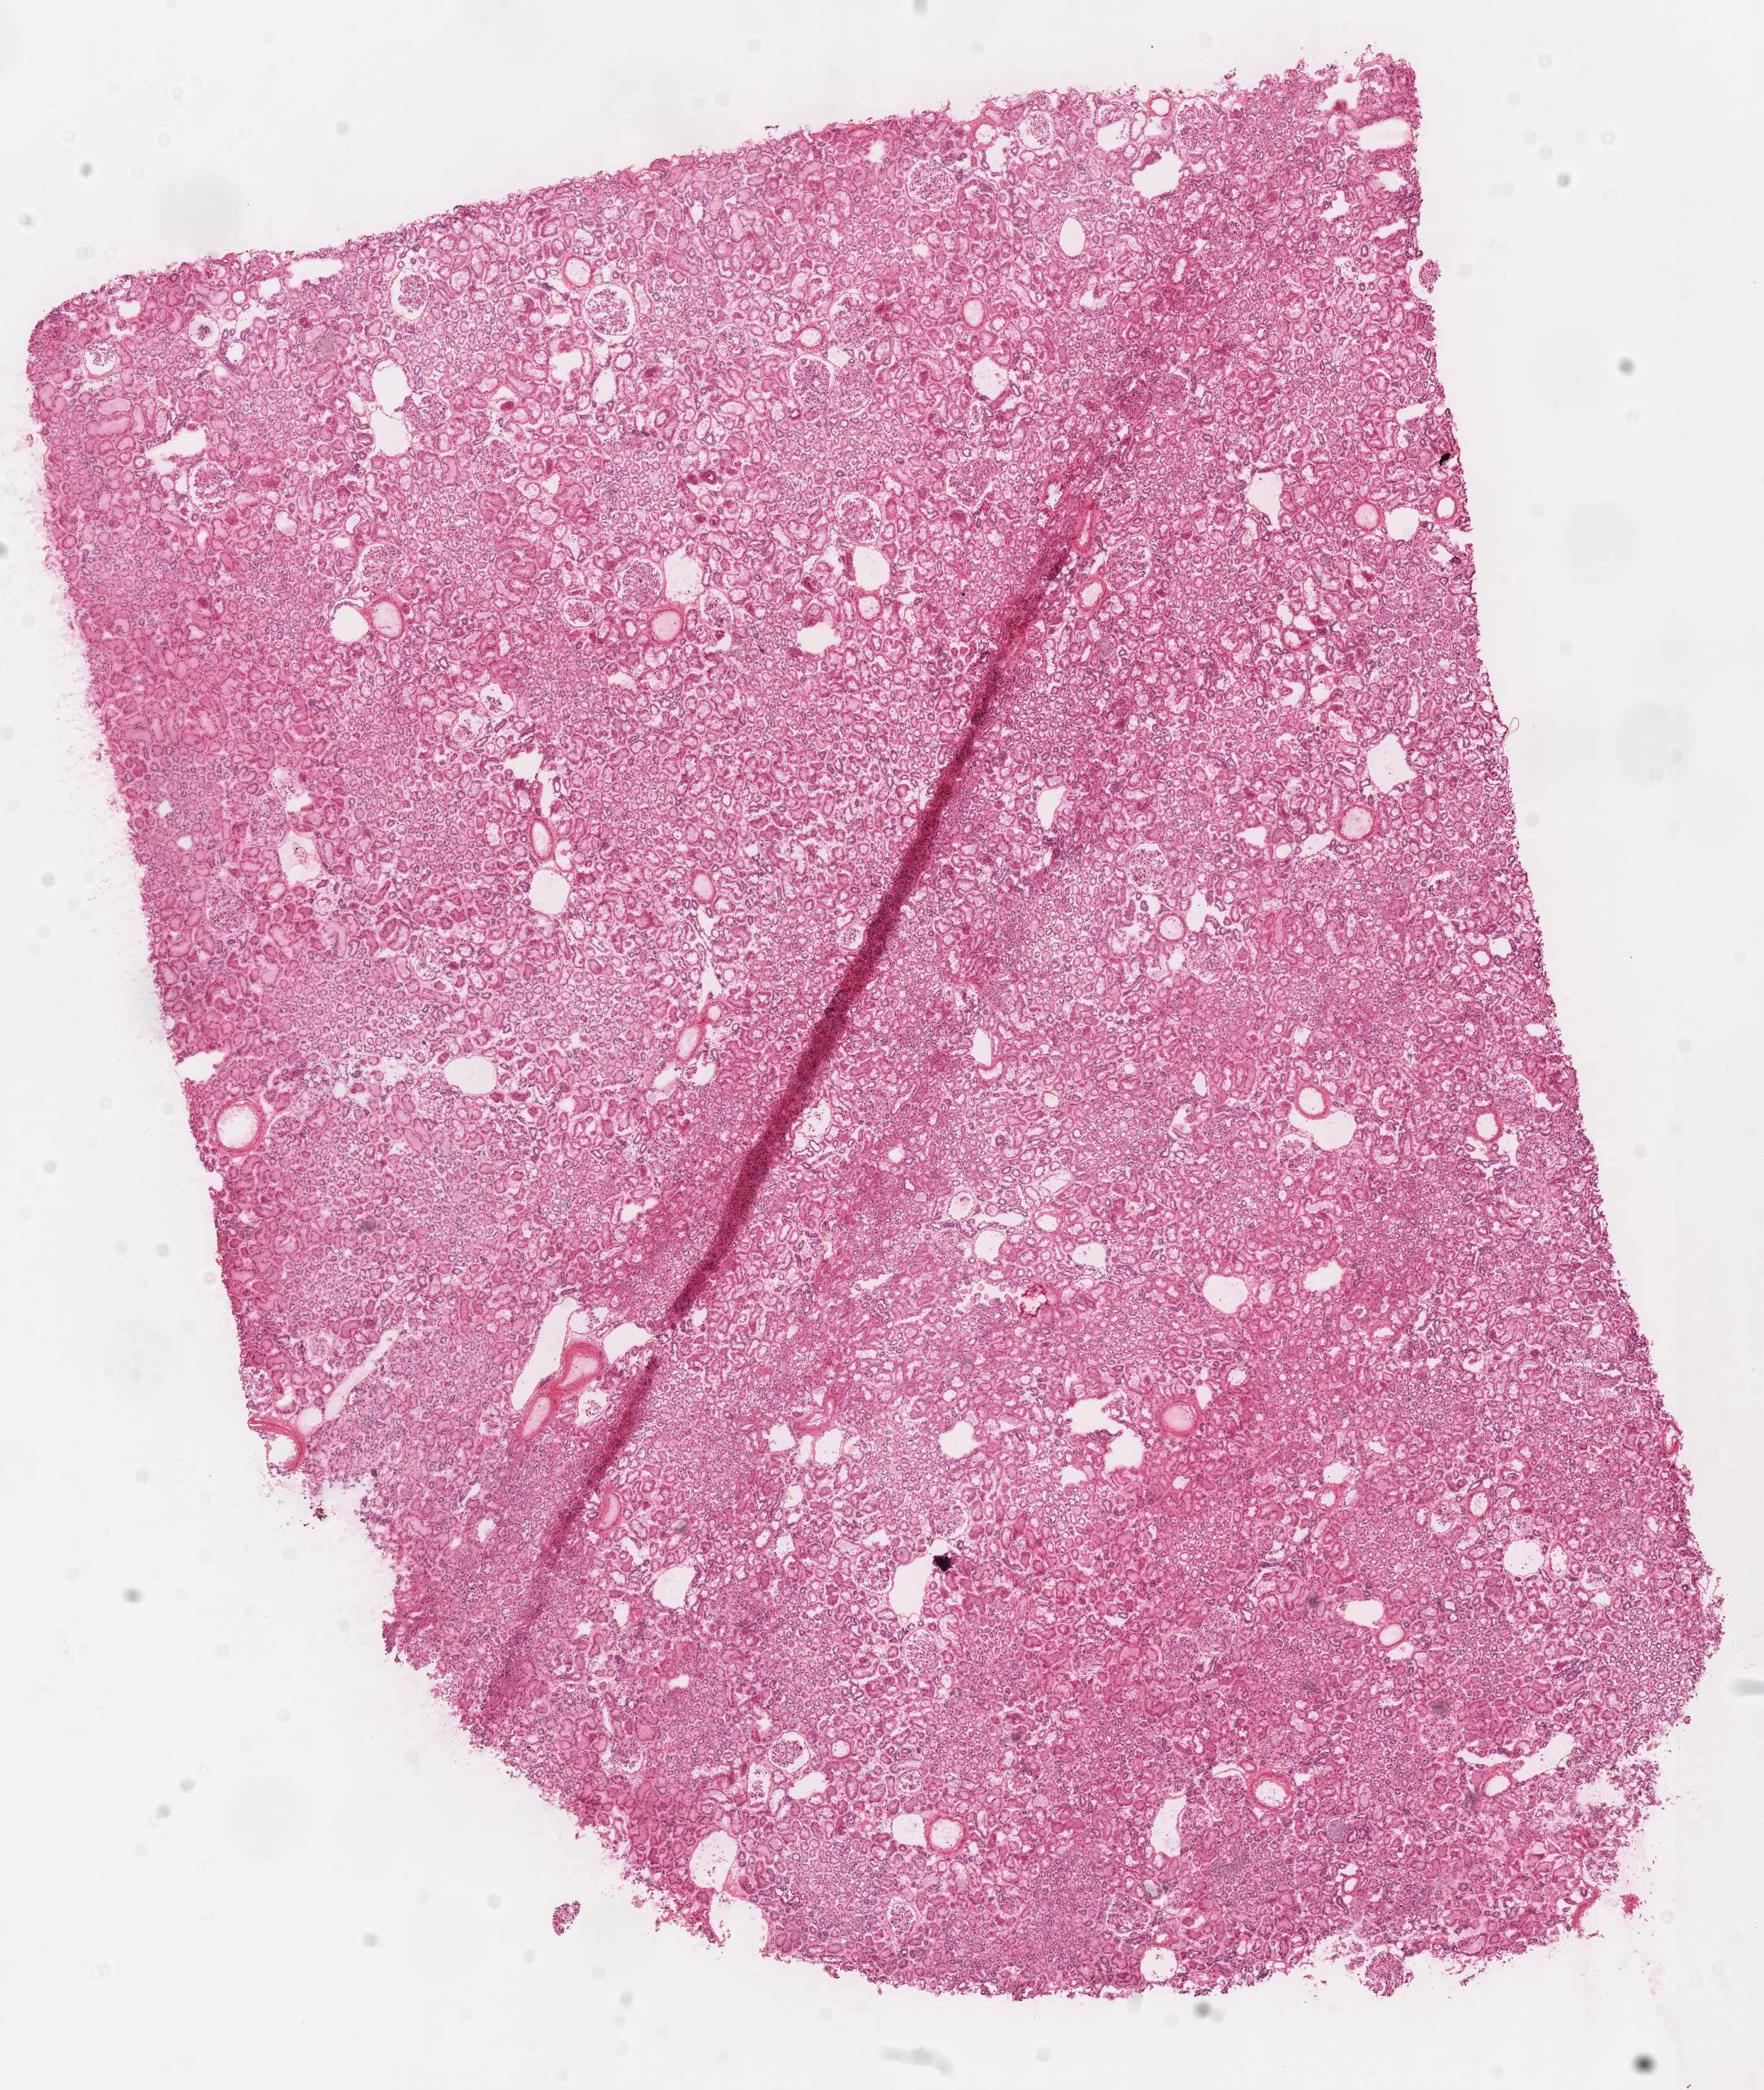
H&E-stained whole-slide image — a low-resolution overview of the entire scanned area, about 9.8 x 11.6 mm, frozen section from the top of the tissue portion, sample: solid tissue normal (non-tumour tissue), kidney. Male, age 34 years at initial diagnosis.
This section: solid tissue normal sample (biorepository sample class). Patient diagnosis: Renal cell carcinoma, chromophobe type.